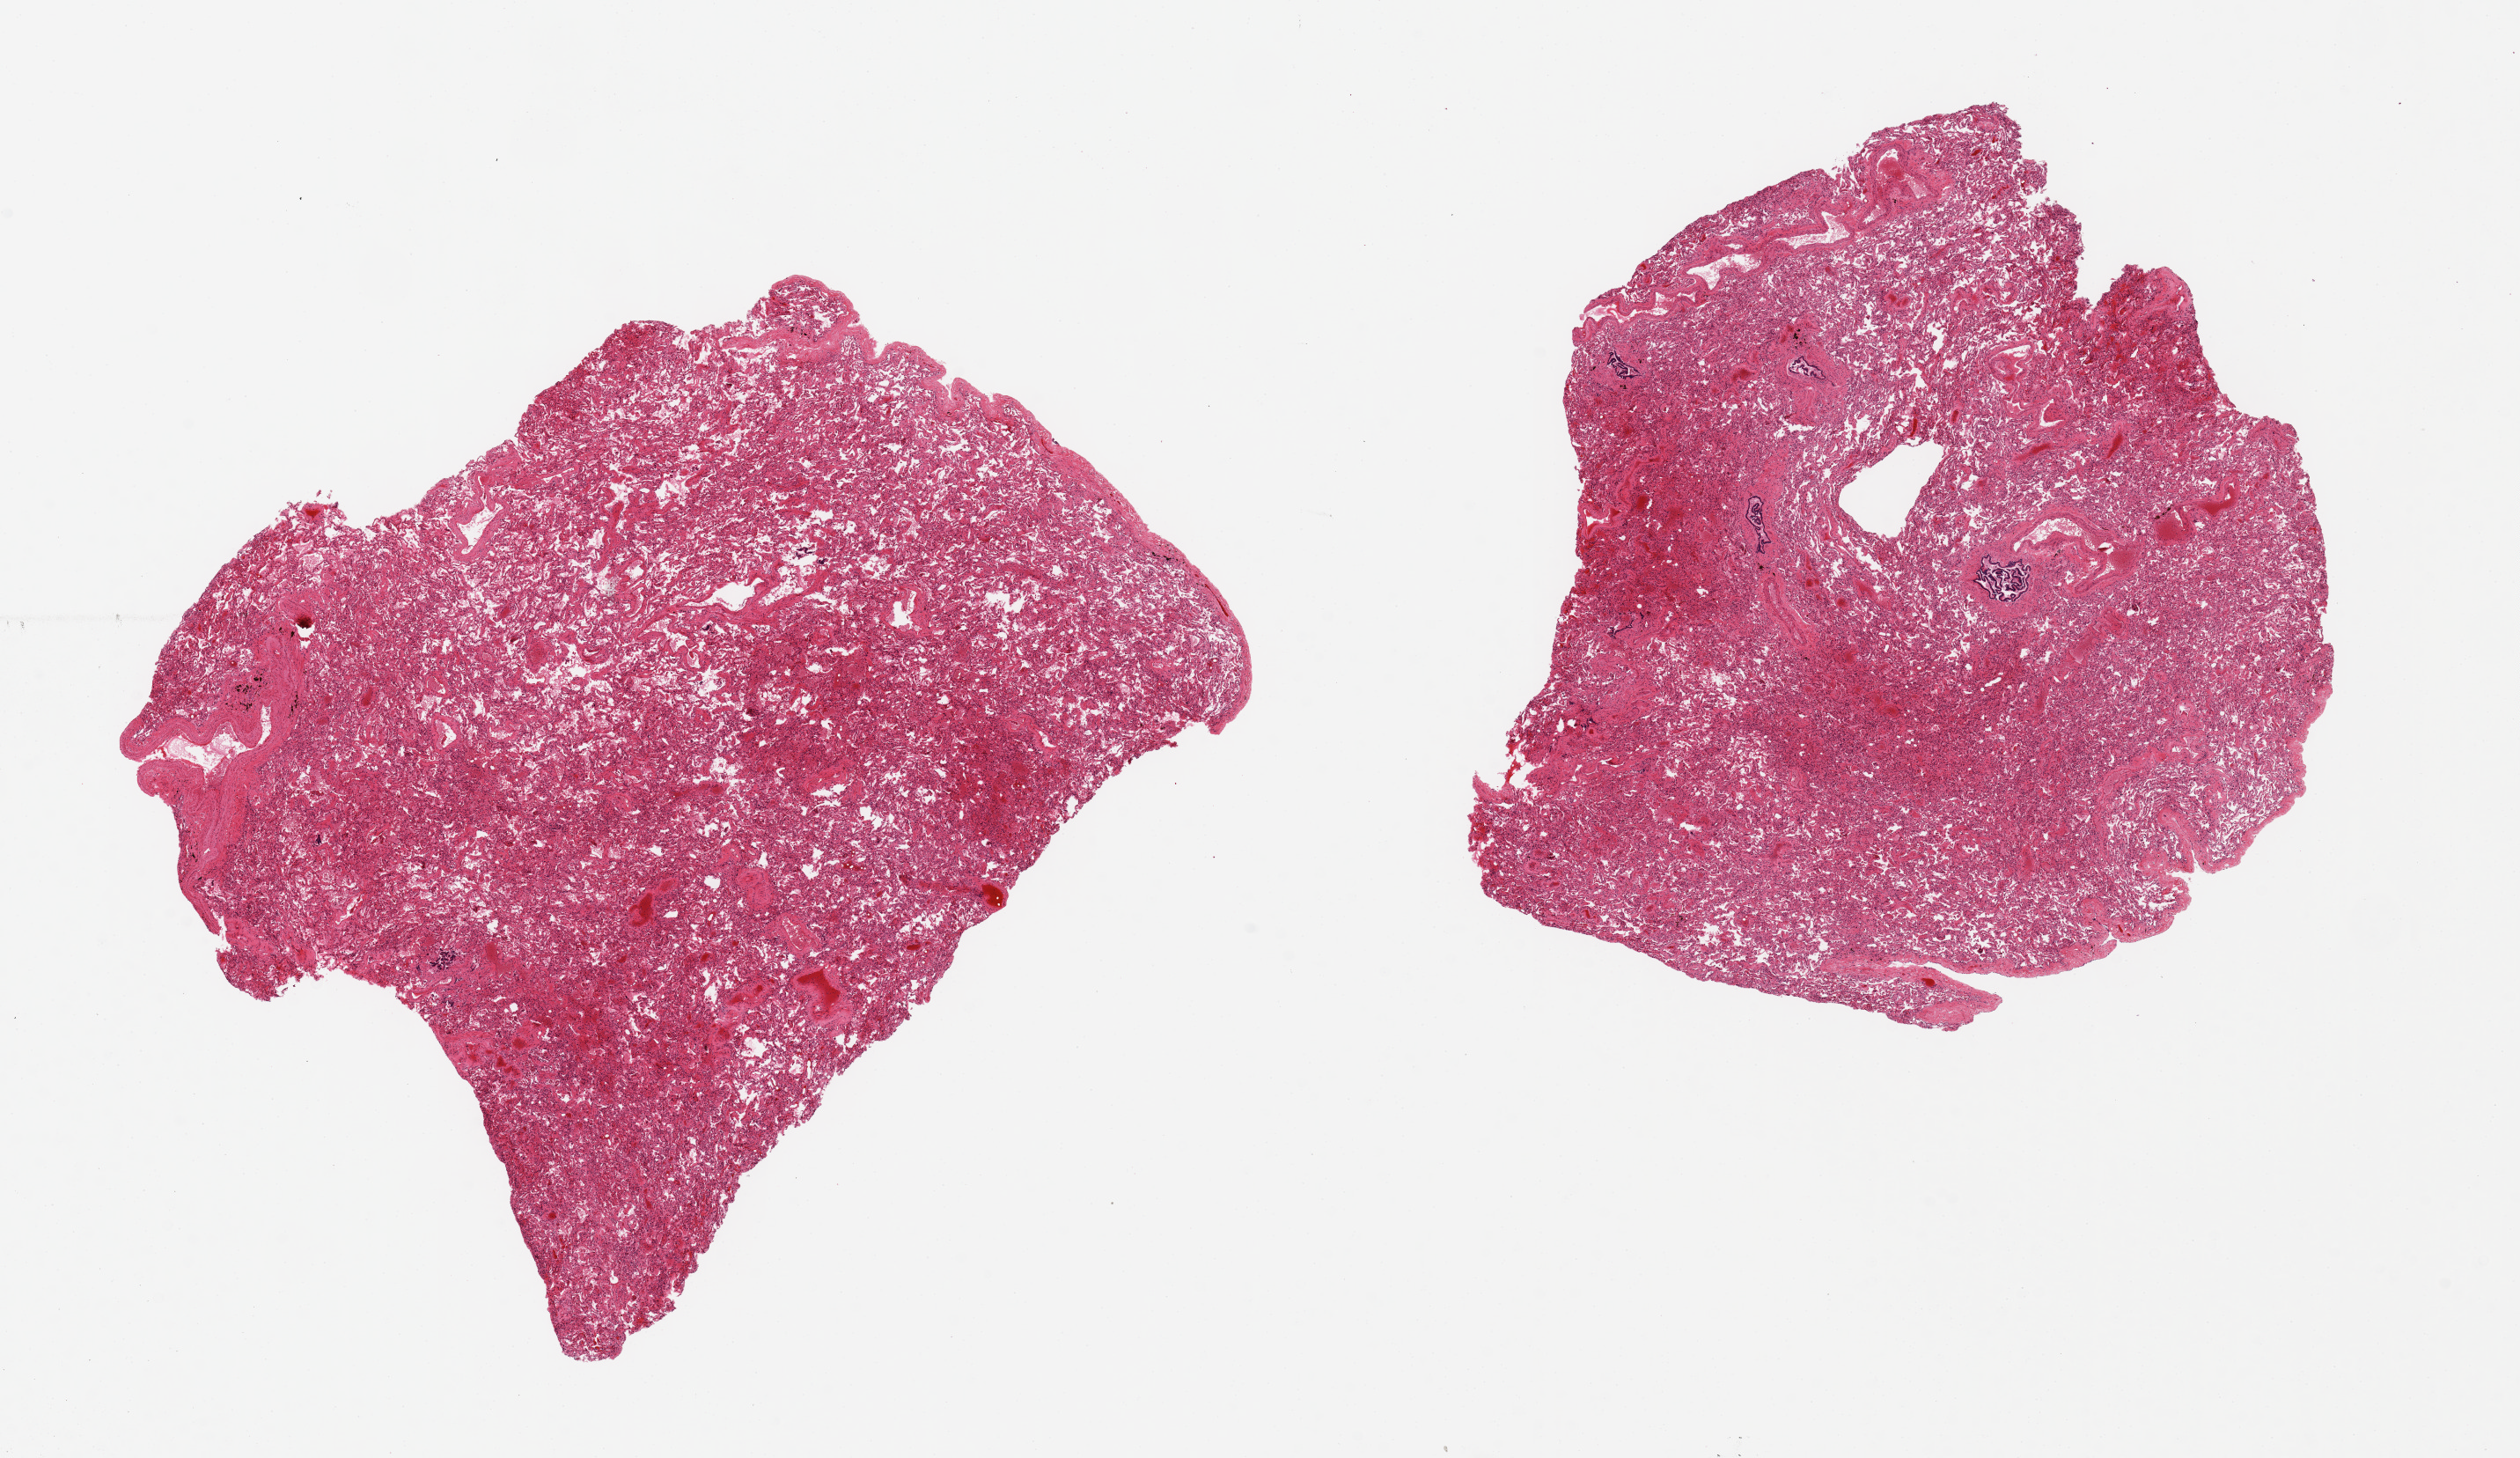
H&E whole-slide image — shown as a low-resolution overview of the whole scanned area (about 22.6 x 13.1 mm). PAXgene-fixed paraffin-embedded (PFPE) section. Section of lung (target tissue). Donor tissue sample. Donor sex: female.
• review note (as recorded): 2 pieces 9x7 & 8x7 mm; moderate alveolar hemorrhages; moderate interstitial fibrosis; no pneumonia or heart failure cells